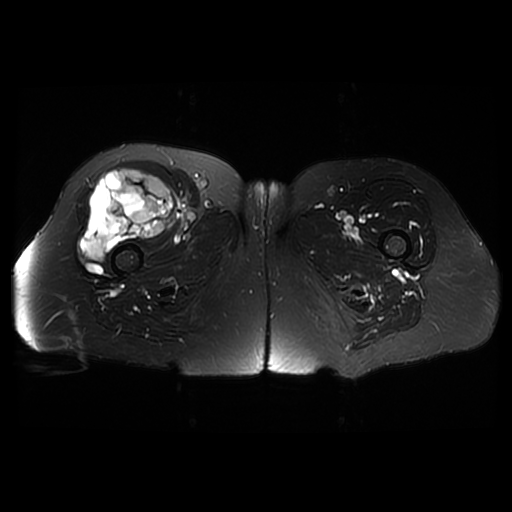
MRI of an extremity soft-tissue mass, one axial slice. Position 28 of 42 along the scan axis. T2-weighted fat-saturated. 6 mm slice thickness. 512 × 512 image matrix, field of view 440 × 440 mm. Female patient. From the clinical record (not read from this slice): histological type: pleiomorphic undifferentiated sarcoma; grade: high; site of the primary tumour: right quadricep.
Annotated regions visible in this slice (outlined manually by an expert reader):
- gross tumour volume including surrounding oedema: bounding box <81,169,173,261> (left, top, right, bottom; pixels)
- gross tumour volume (mass): <81,169,173,261>